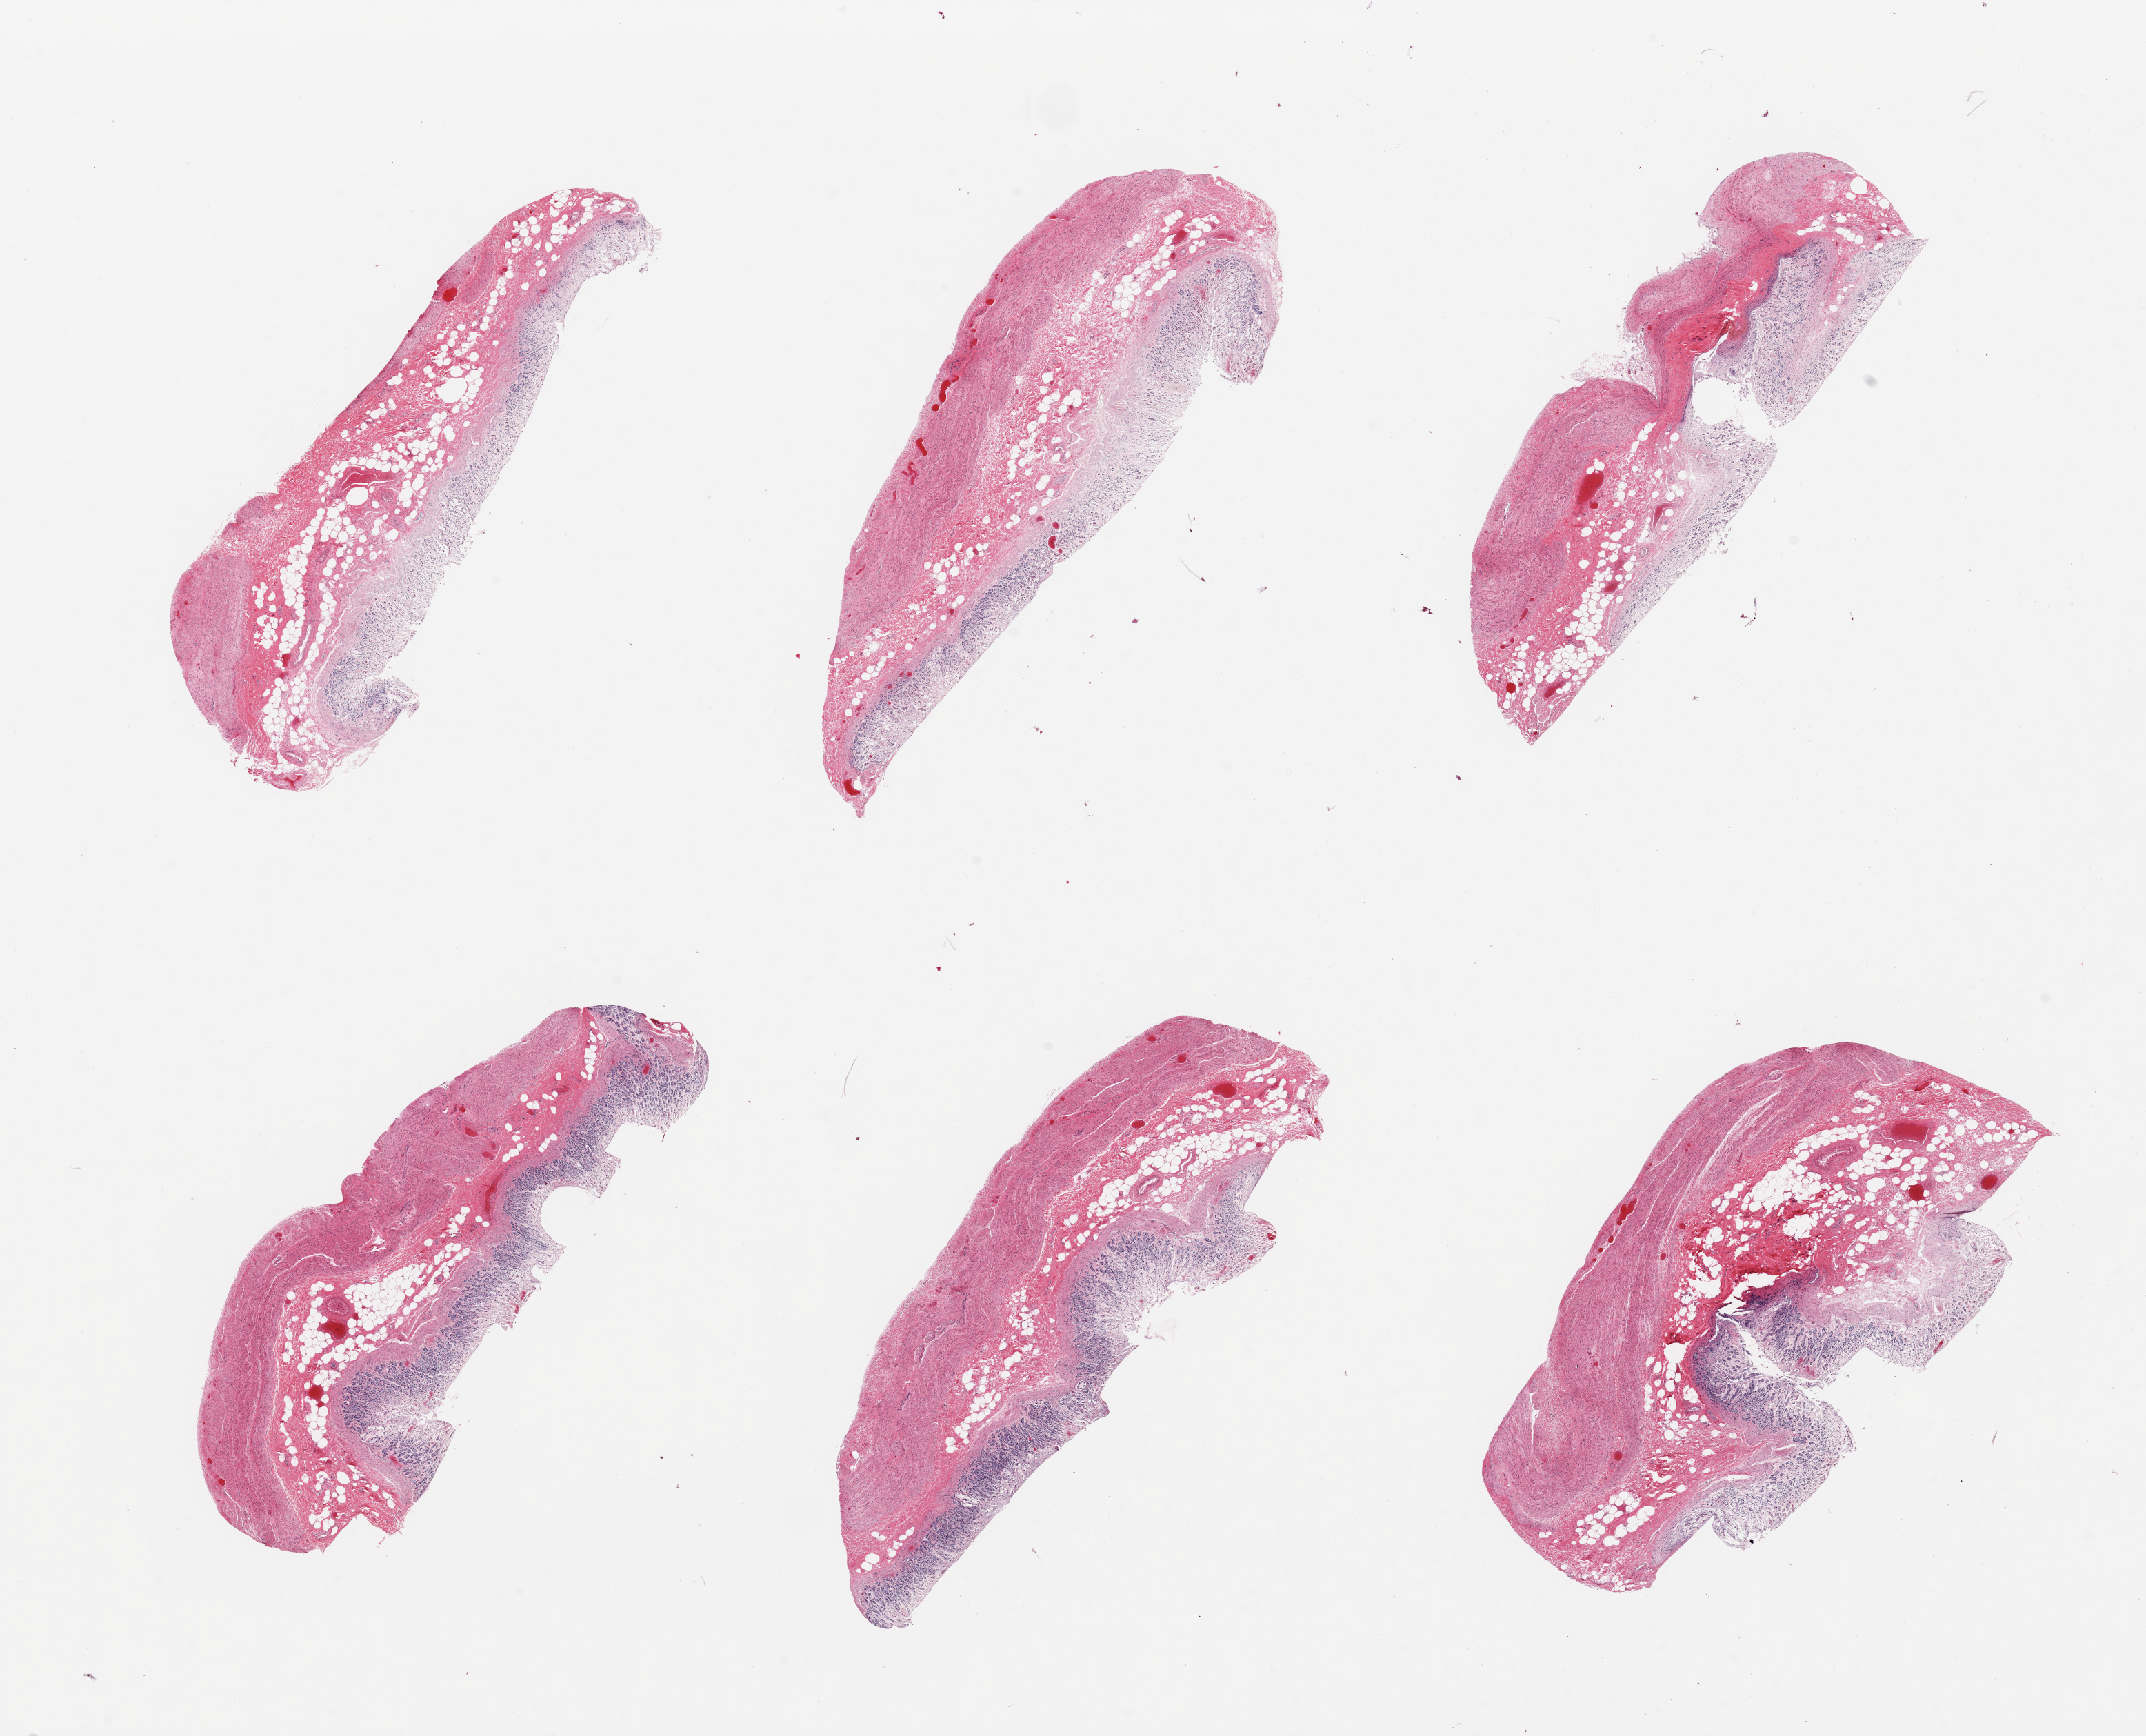
Digitized haematoxylin and eosin-stained section — low-resolution overview of the scanned area, about 24.6 x 19.9 mm (slide scanned at 20x), PAXgene-fixed, paraffin-embedded tissue, target tissue: stomach, donor tissue sample.
Pathologist's review note for this sample: 6 pieces, severely autolyzed mucosa.